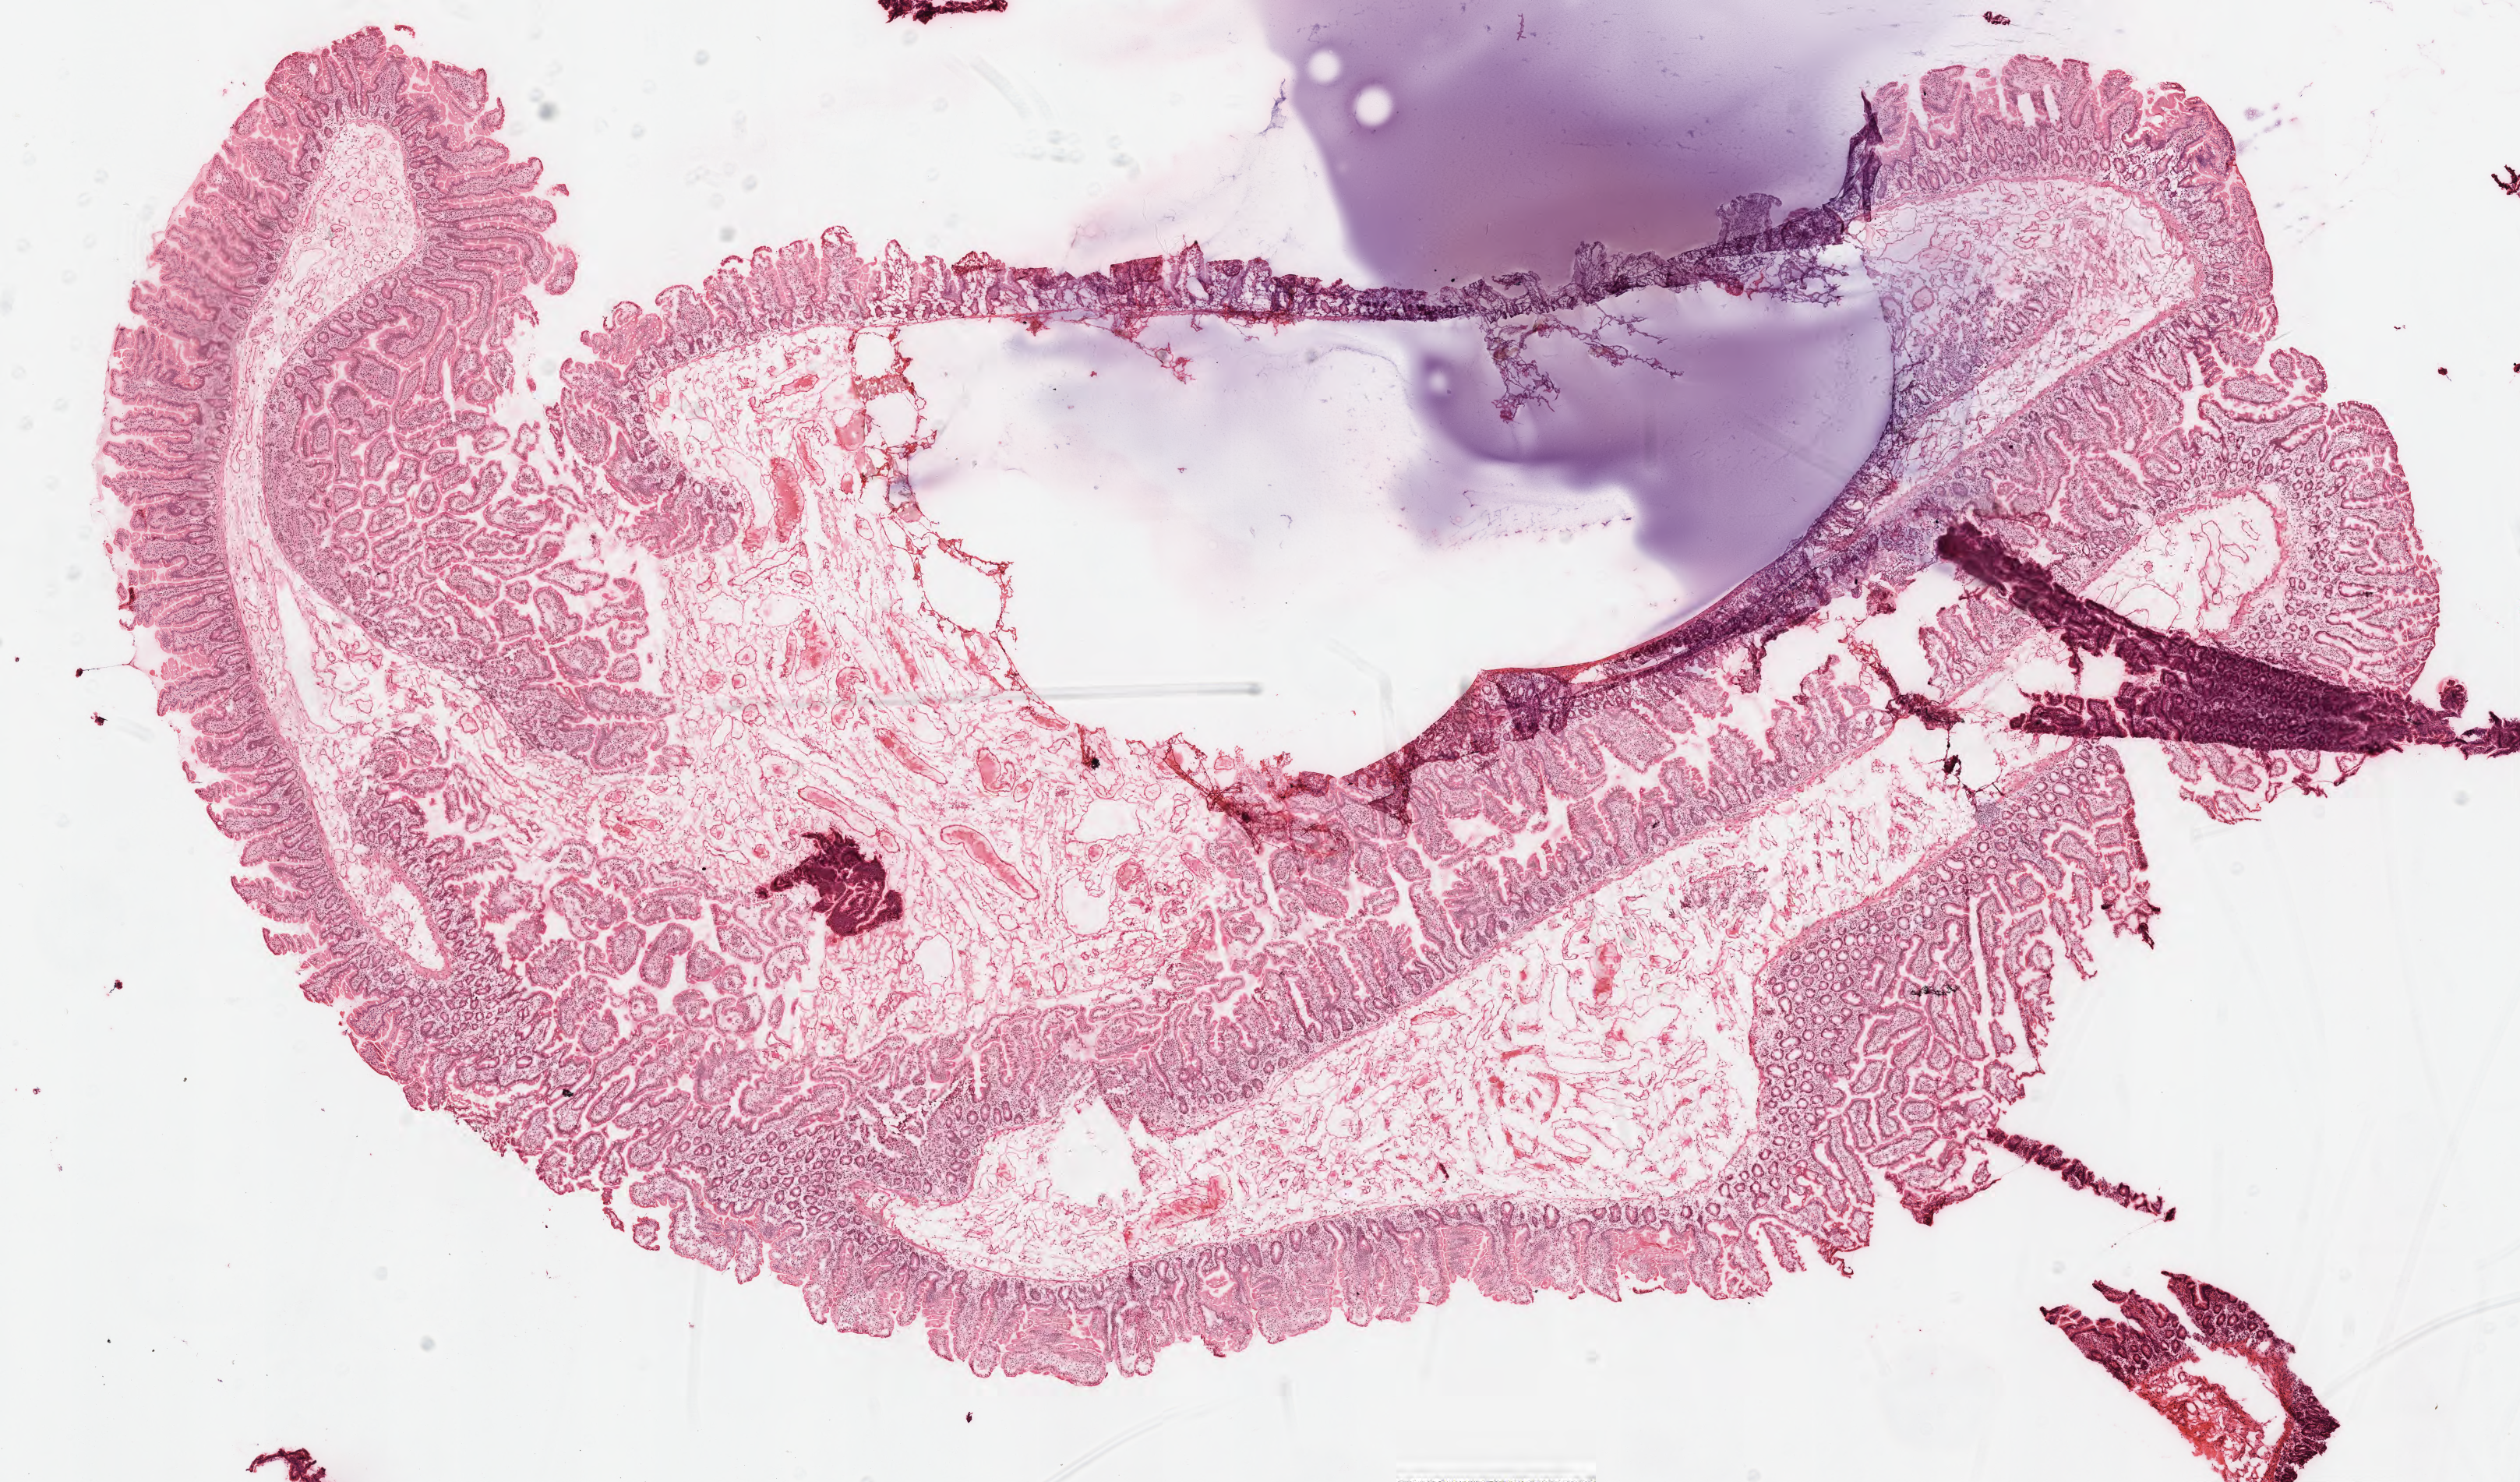
Hematoxylin and eosin (H&E) whole-slide image — a low-resolution overview of the entire scanned area, about 12.7 x 7.5 mm, frozen section, non-tumor (normal tissue) sample from a patient with adenocarcinoma, NOS, anatomic site: extrahepatic bile duct. Male, age 52 years at initial diagnosis. Pathologist review of this section (percent, as recorded): tumor cells 0%, tumor nuclei 0%, stromal cells 0%, necrosis 0%, normal cells 100%. Infiltration values recorded for this section: lymphocyte infiltration 0%, monocyte infiltration 0%, neutrophil infiltration 0%.
This section: non-tumor tissue sample; the patient's diagnosis is given above. Section: top of the tissue portion.